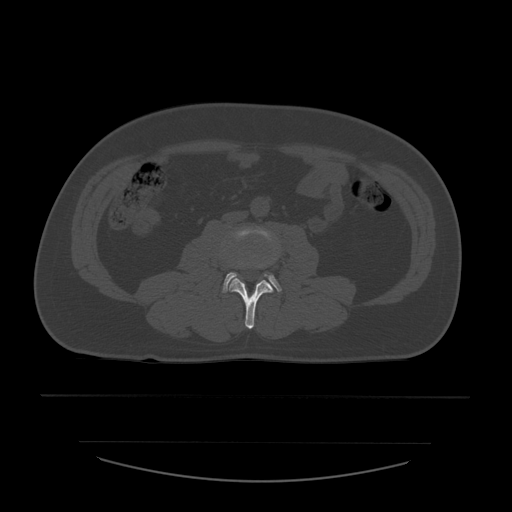
CT including the spine, one axial slice; position 163 of 532 along the scan axis; reconstruction kernel STANDARD; 120 kVp; bone window (W 1800 / L 400 HU); 512 × 512 image matrix, field of view 441 × 441 mm. Patient age 44 years. From the clinical record (not read from this slice): primary cancer: soft tissue sarcoma.
Structures marked on this image (semi-automatic segmentation, software-assisted and operator-edited):
- L3 vertebra: box from (x=229, y=228) to (x=278, y=329) px
- L4 vertebra: (x=223, y=267)–(x=282, y=292)